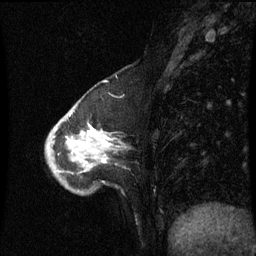
Breast MRI (dynamic contrast-enhanced), one sagittal slice; position 21 of 60 along the scan axis; dynamic contrast-enhanced series, image 2 of 3 at this slice position (ordered by acquisition); 1.5 T; TE 4.2 ms, TR 8.9 ms; 2 mm slice thickness; 256 × 256 image matrix, field of view 200 × 200 mm. Patient: female, 50 years. Case-level facts recorded for this patient, not image findings: setting: breast cancer imaged before/during neoadjuvant chemotherapy; receptor status: HR-positive, HER2-negative.
Structures marked on this image (semi-automatically segmented with operator editing):
- analysis volume of interest (the breast-tissue region the enhancement analysis was run in; not a lesion): bounding box [x1, y1, x2, y2] px = [47, 100, 124, 195]
- tumour enhancement mask (voxels above the 70 % enhancement threshold inside the analysis volume of interest): [88, 128, 111, 163]